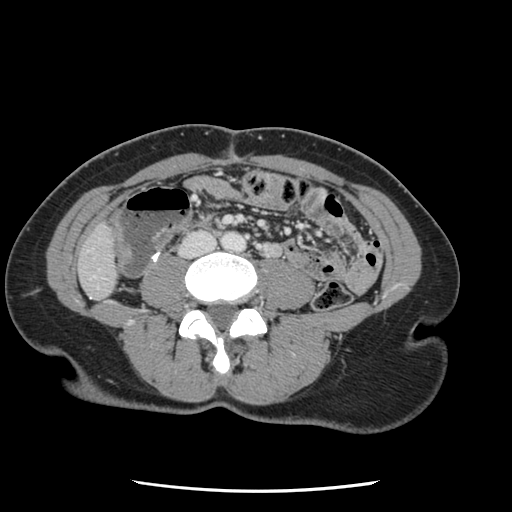
Contrast-enhanced abdominal CT, one axial slice; position 4 of 134 along the scan axis; intravenous contrast given; soft-tissue window (W 400 / L 40 HU); 512 × 512 image matrix. Female patient, age 43 years. Case-level facts recorded for this patient, not image findings: diagnosis: colorectal cancer liver metastases, imaged before liver resection; multiple liver metastases: yes; largest metastasis: 3.4 cm; disease in both lobes: yes.
Annotated regions visible in this slice (outlined manually by an expert reader):
- liver: bounding box (x1, y1, x2, y2) in pixels: (80, 226, 117, 299)
- planned liver remnant (the part of the liver to remain after resection): (80, 227, 117, 300)